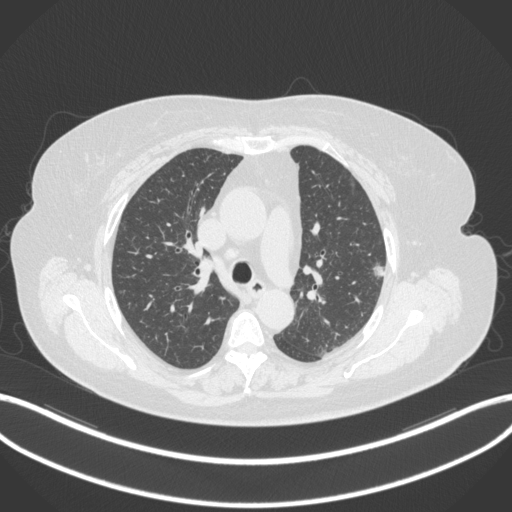
Chest CT, one axial slice. Slice 216 of 310 in the series (ordered by position). Lung window (W 1500 / L -600 HU). 1 mm slice thickness. 512 × 512 image matrix. Female patient, age 70 years. From the clinical record (not read from this slice): clinical TNM (as recorded): T1c N0 M0.
Annotated regions visible in this slice (rectangle marked by the reading radiologist):
- lung tumour (recorded histology: adenocarcinoma): bounding box (x1, y1, x2, y2) in pixels: (371, 258, 387, 282)